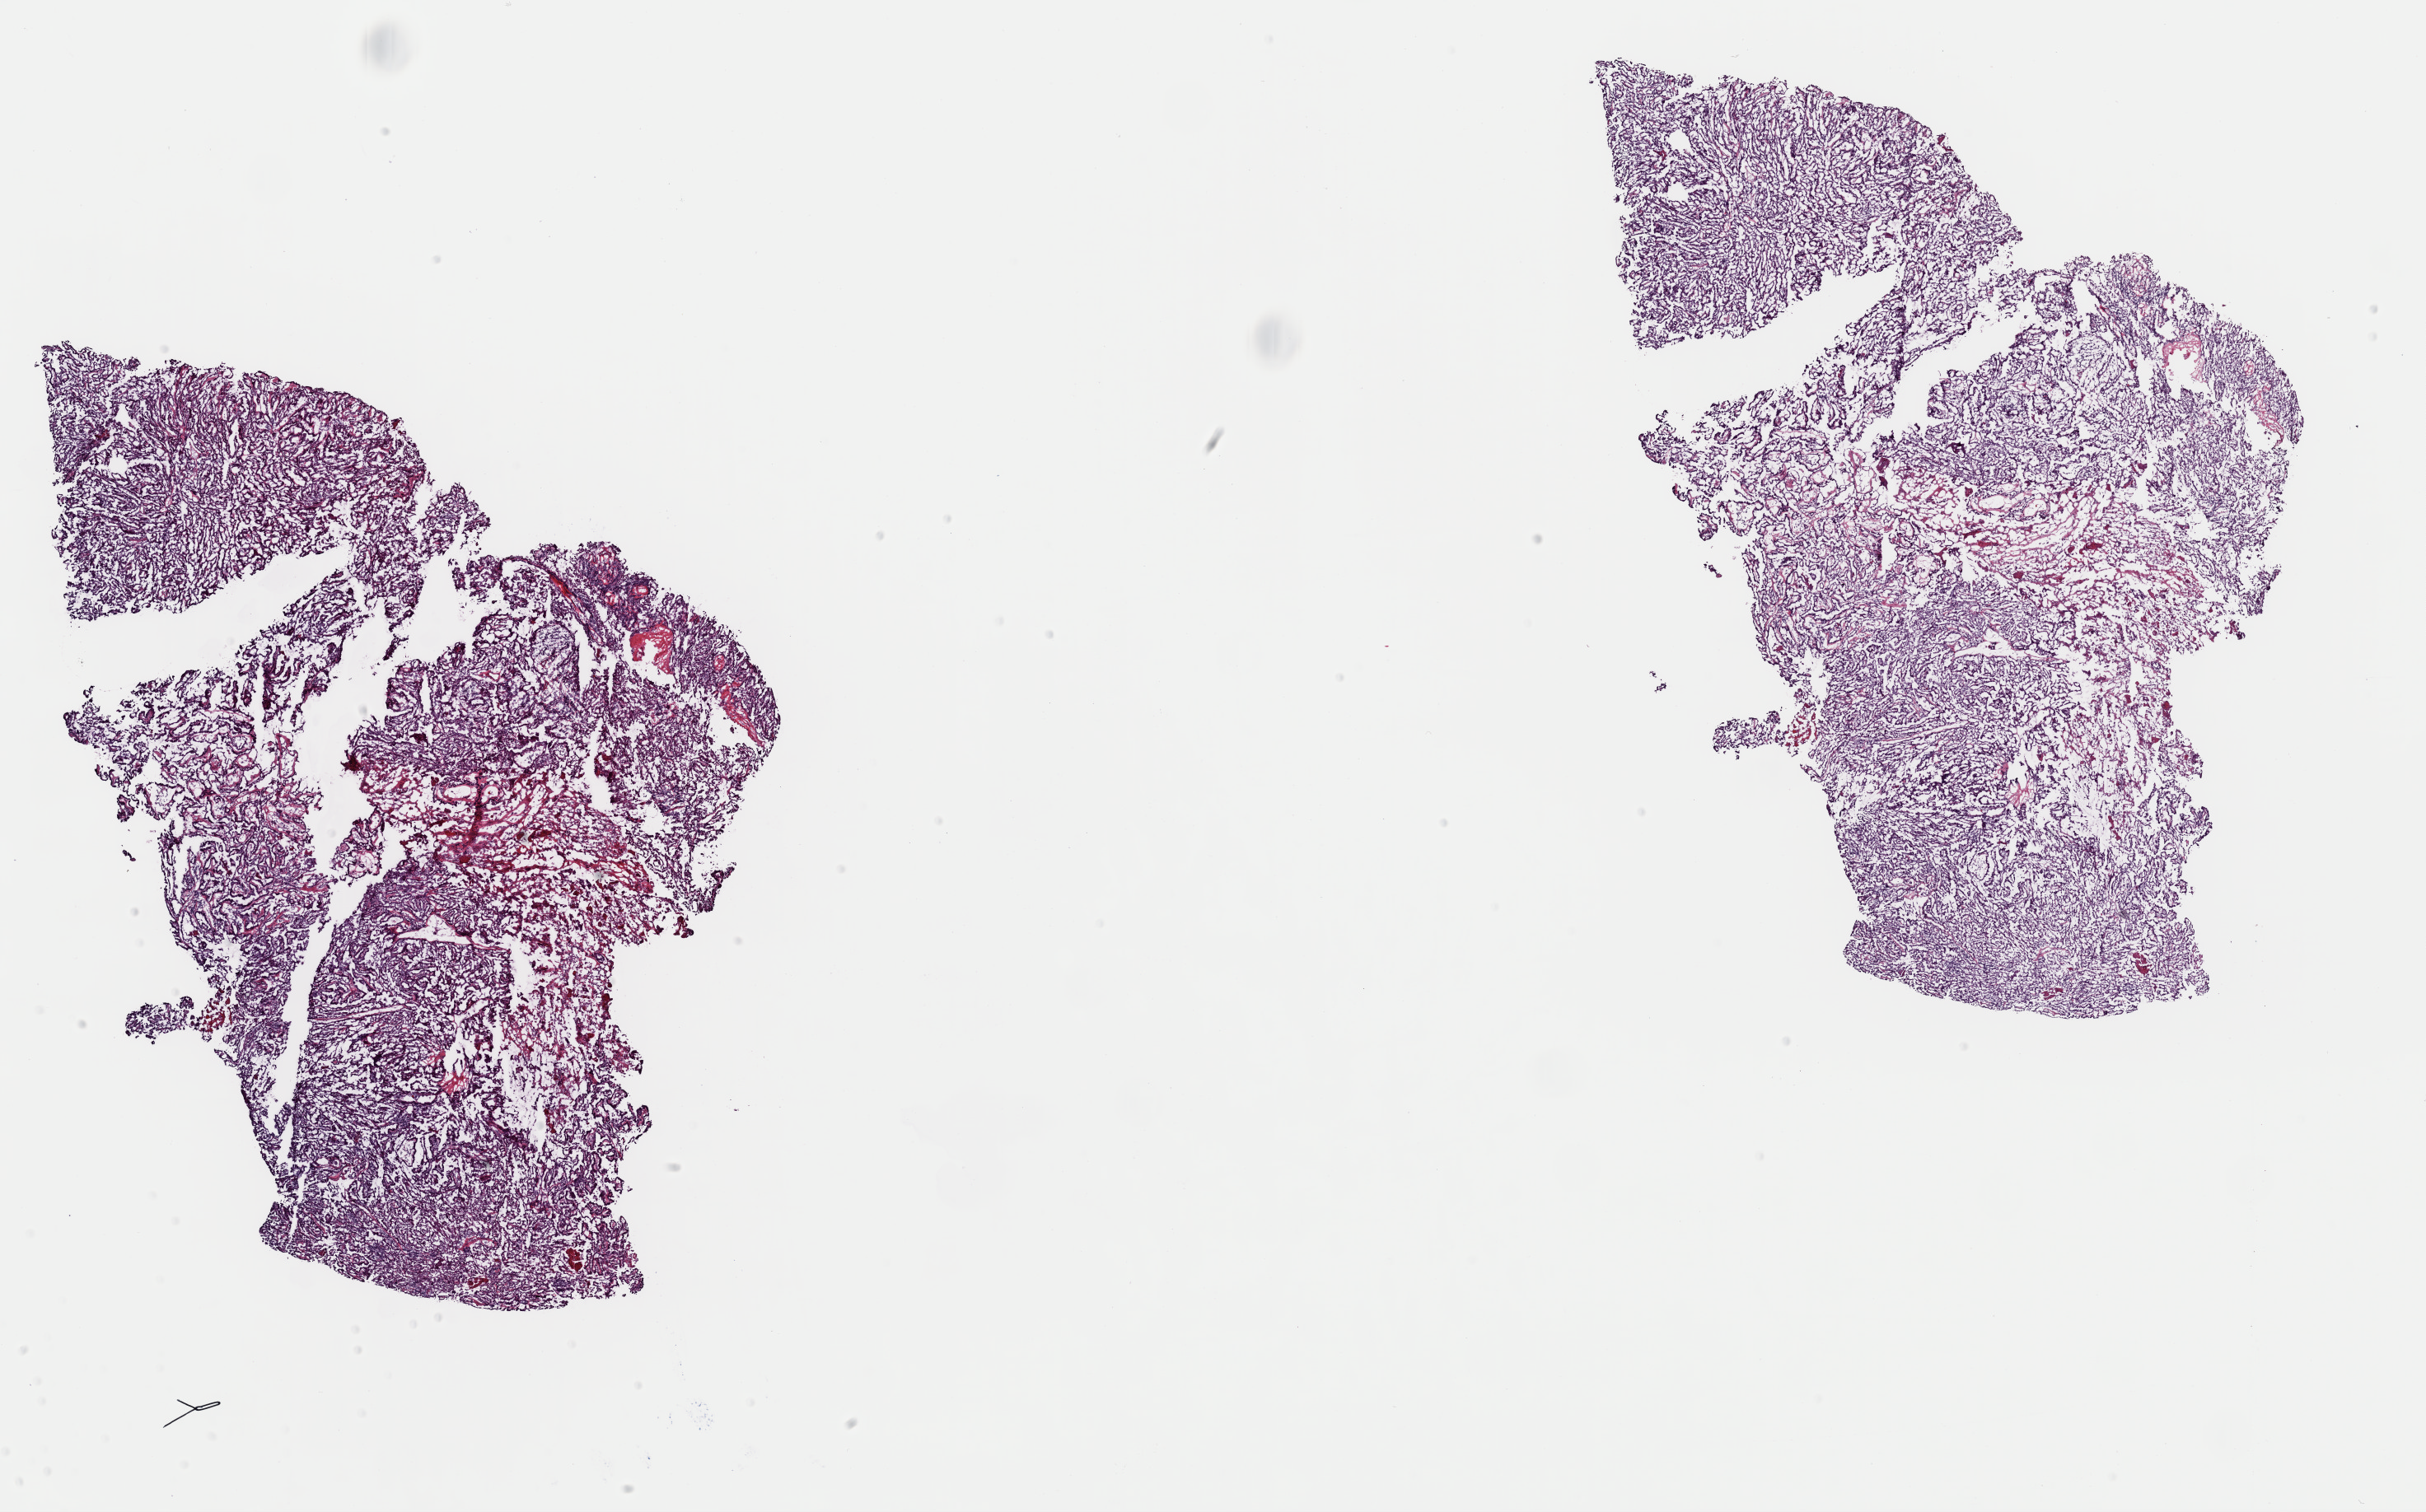
Whole-slide histology image, Hematoxylin and eosin (H&E) stained, shown as a low-resolution overview of the whole scanned area (about 23.3 x 14.5 mm, slide scanned at 40x), frozen section from the top of the tissue portion, primary tumour sample from the thyroid. Patient: female, age at initial diagnosis 34 years. Pathologist review of this section (percent, as recorded): tumour cells 100%, tumour nuclei 90%, normal cells 0%, stromal cells 0%, necrosis 0%. Inflammatory infiltration, as recorded: lymphocyte infiltration 0%, monocyte infiltration 0%, neutrophil infiltration 0%.
TNM: T3 N0 M0. Laterality: left. Diagnosis: Papillary adenocarcinoma, NOS (thyroid gland). AJCC pathologic stage: I.